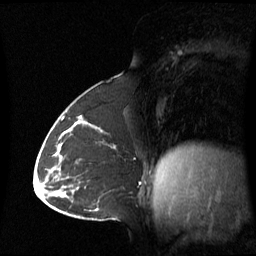
Breast MRI (dynamic contrast-enhanced), one sagittal slice. Position 30 of 60 along the scan axis. Dynamic contrast-enhanced series, image 2 of 3 at this slice position (ordered by acquisition). 1.5 T. TE 4.2 ms, TR 8.4 ms. 256 × 256 image matrix, field of view 270 × 270 mm. Female patient, age 43 years. Case-level facts recorded for this patient, not image findings: setting: breast cancer imaged before/during neoadjuvant chemotherapy; receptor status: triple-negative.
Outlined on this slice (semi-automatic segmentation, software-assisted and operator-edited):
- analysis volume of interest (the breast-tissue region the enhancement analysis was run in; not a lesion): bounding box <62,124,115,180> (left, top, right, bottom; pixels)
- tumour enhancement mask (voxels above the 70 % enhancement threshold inside the analysis volume of interest): <62,131,65,135>